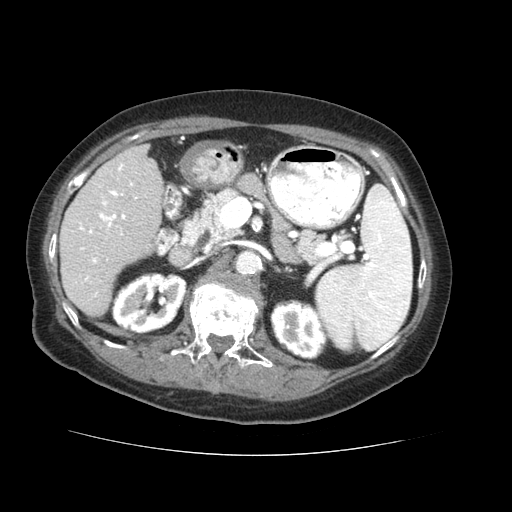
Contrast-enhanced abdominal CT (liver protocol), one axial slice. Slice 22 of 73 in the series (ordered by position). Reconstruction kernel STANDARD. Soft-tissue window (W 400 / L 40 HU). 512 × 512 image matrix. Case-level facts recorded for this patient, not image findings: diagnosis: hepatocellular carcinoma (patient treated with transarterial chemoembolisation; whether this scan precedes or follows treatment is not stated here); TNM stage (as recorded): Stage-IVB; Child-Pugh class: A; tumour differentiation: well differentiated; tumour nodularity: uninodular.
Structures marked on this image (semi-automatic segmentation, software-assisted and operator-edited):
- liver parenchyma outside the tumour (the mass and vessels are separate outlines, so this box may not span the whole liver): bounding box (x1, y1, x2, y2) in pixels: (60, 144, 162, 316)
- liver vessels: (78, 163, 146, 297)